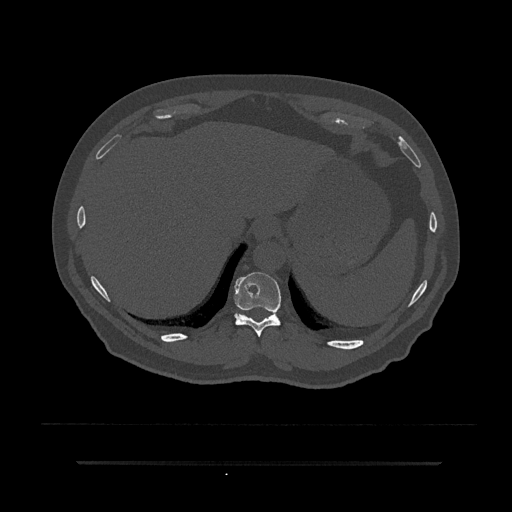
CT including the spine, one axial slice; 120 kVp; bone window (W 1800 / L 400 HU); 512 × 512 image matrix. Male patient, age 59 years. From the clinical record (not read from this slice): primary cancer: bile ducts; vertebrae with lytic lesions (as recorded): T10.
Annotated regions visible in this slice (semi-automatic segmentation, software-assisted and operator-edited):
- T10 vertebra: bounding box [x1, y1, x2, y2] px = [234, 272, 281, 337]
- T11 vertebra: [236, 313, 249, 318]